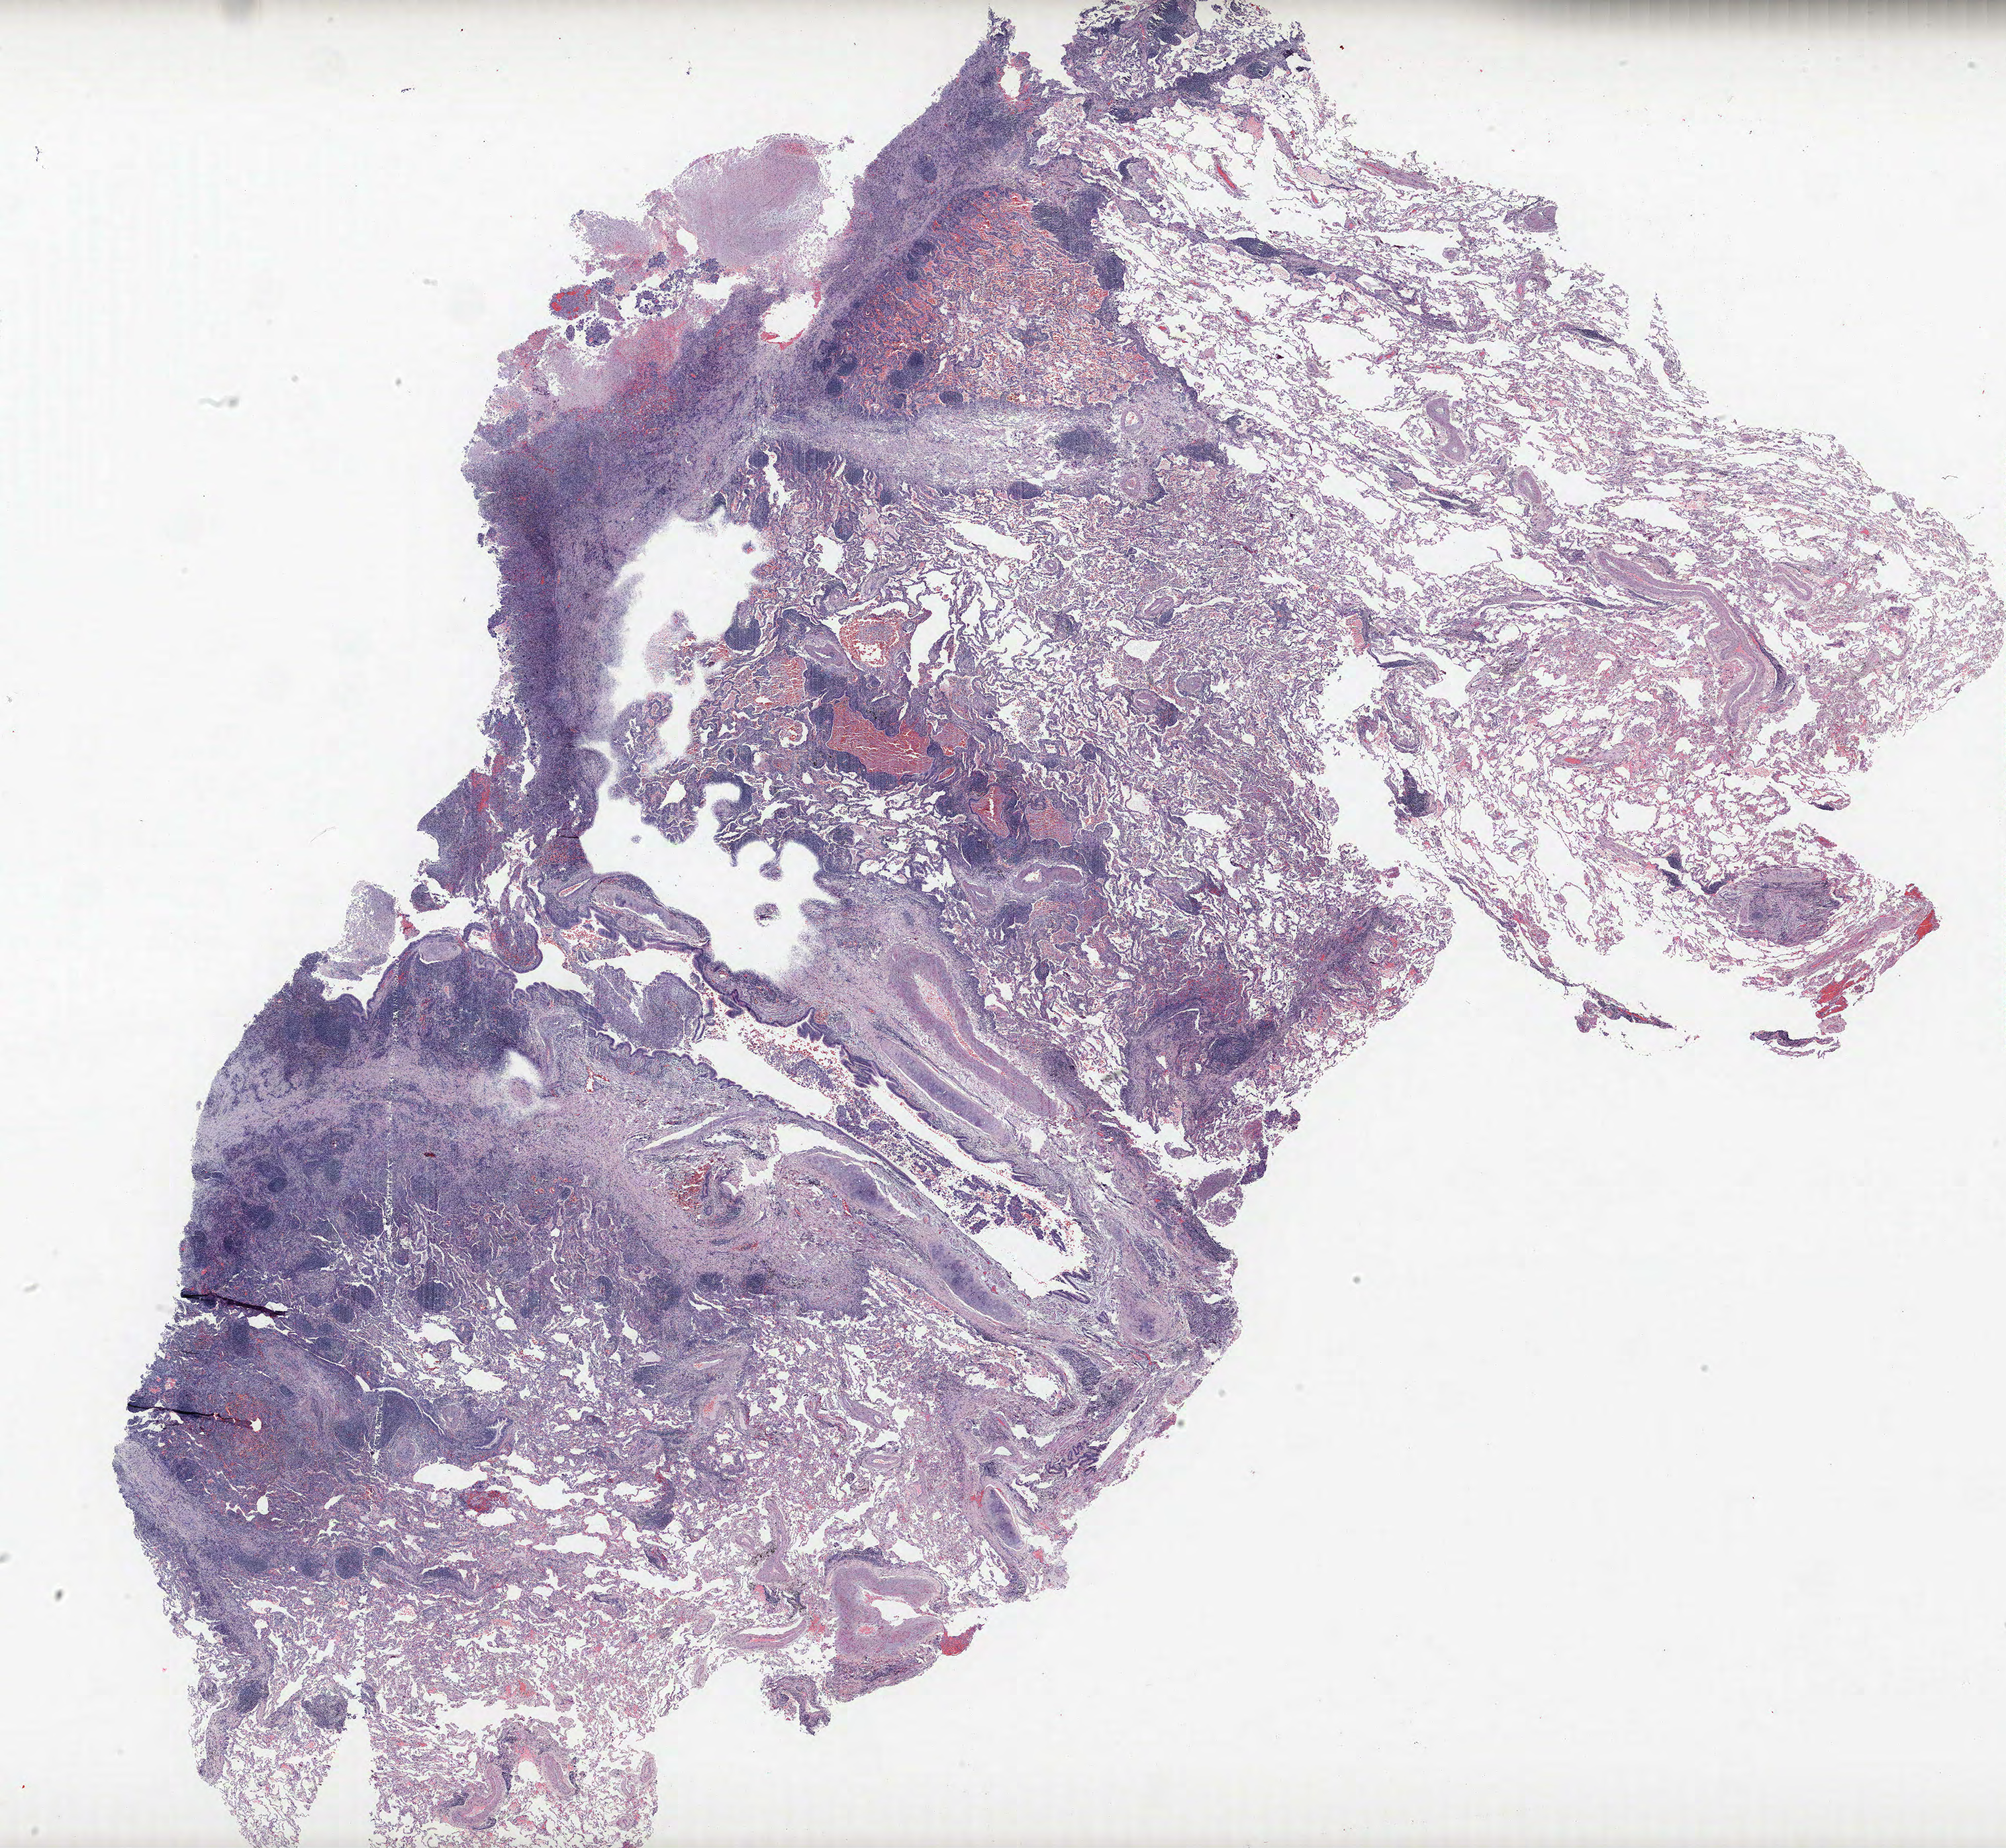
Whole-slide histology image, H&E-stained — a low-resolution overview of the entire scanned area, about 24.2 x 22.3 mm (slide scanned at 40x), formalin-fixed paraffin-embedded (FFPE) section, lung. Male, age 63 at enrolment. Former smoker at enrolment. Grade: undifferentiated (G4).
Participant's lung-cancer diagnosis: Large cell carcinoma, NOS. Primary tumour location (clinical record): right upper lobe. Stage (AJCC 6th edition): IB. Tumour size (pathology): 45 mm.